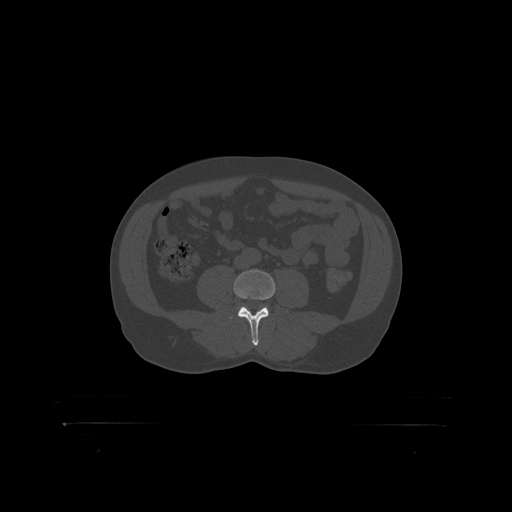
CT including the spine, one axial slice. Slice 230 of 399 in the series (ordered by position). Reconstruction kernel STANDARD. Bone window (W 1800 / L 400 HU). 1.25 mm slice thickness. 512 × 512 image matrix, field of view 650 × 650 mm. Patient: male, 46 years. Case-level facts recorded for this patient, not image findings: primary cancer: skin.
Structures marked on this image (semi-automatically segmented with operator editing):
- L4 vertebra: bounding box <234,270,276,319> (left, top, right, bottom; pixels)